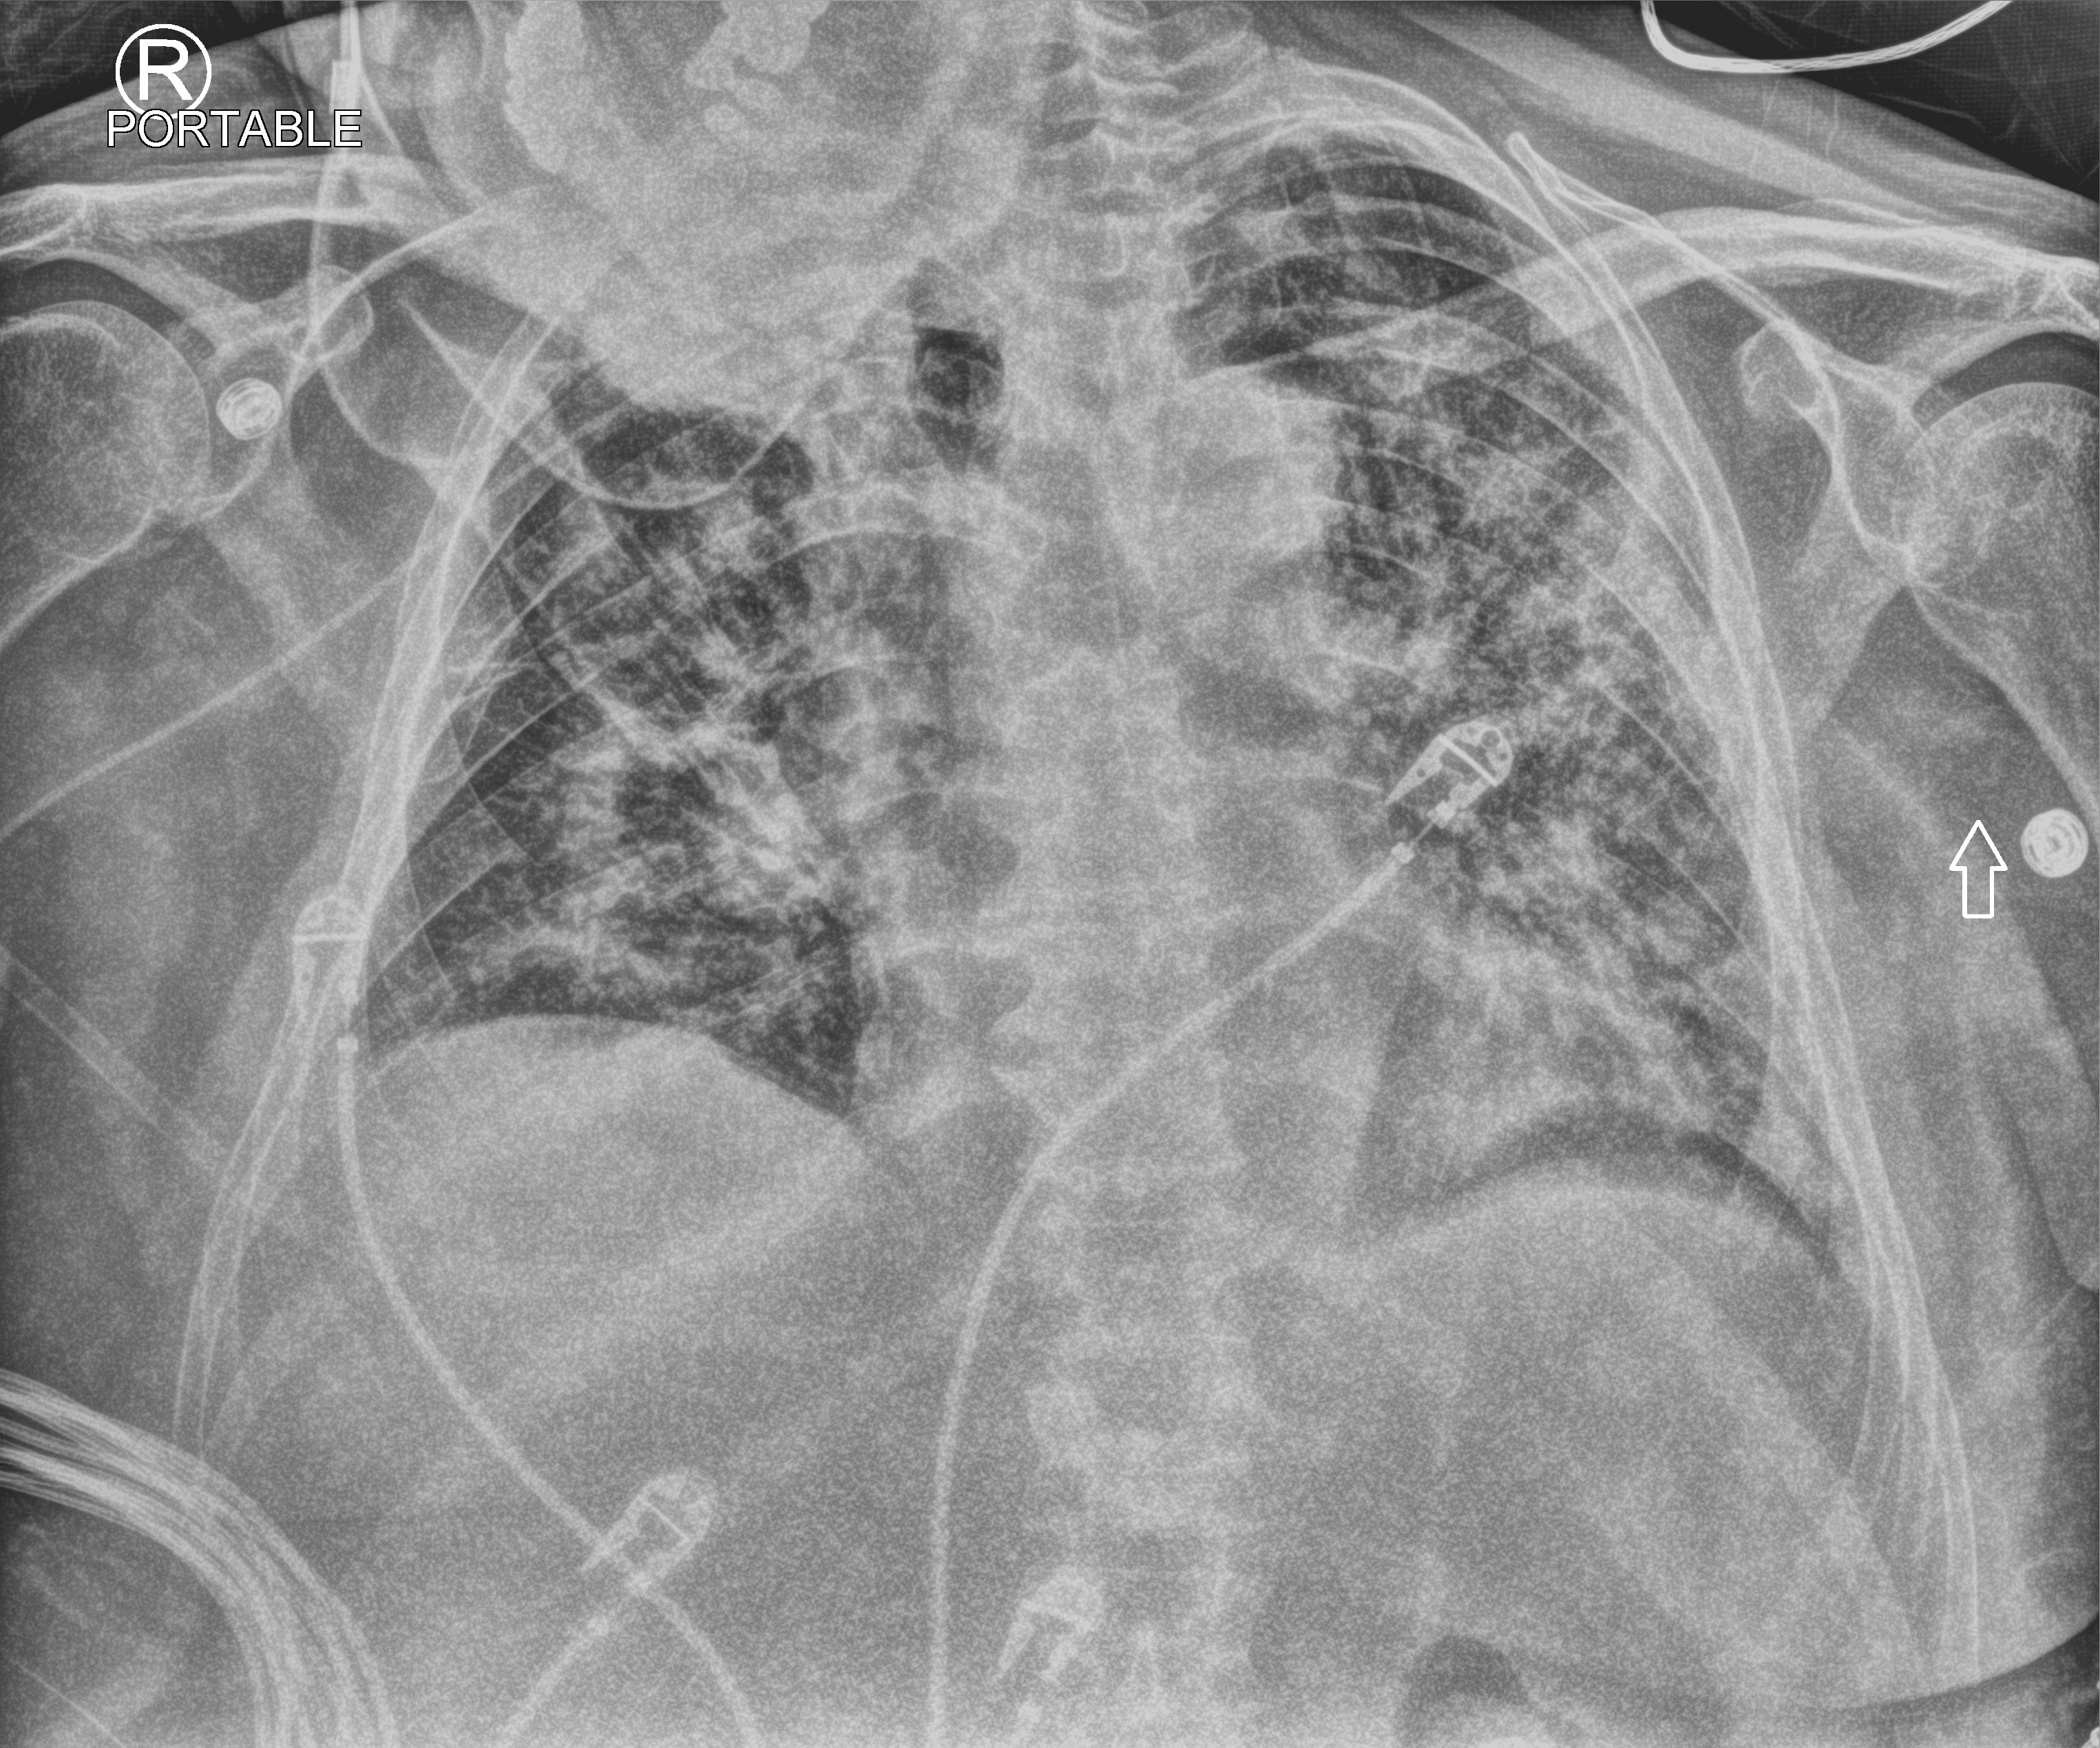
Bedside chest radiograph (computed radiography); anteroposterior (AP) projection. Patient hospitalised with COVID-19; male, aged 60–74 years.
Admission-level facts for this patient (not findings on this image; timing relative to this image not recorded): length of hospital stay: 24 days.